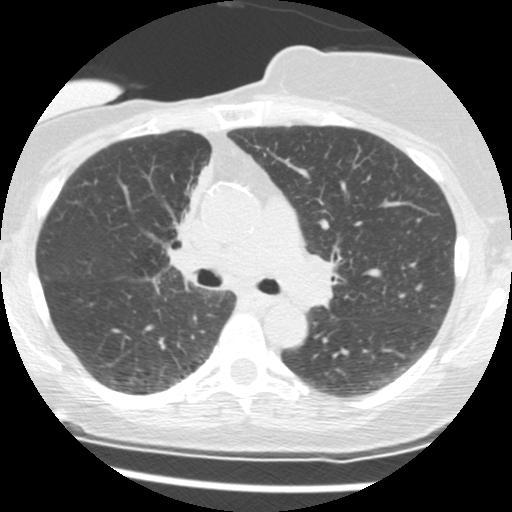
Chest CT (low-dose screening protocol), one axial image, second annual screen, lung window (W 1500 / L -600 HU), 2.5 mm slice thickness, standard (soft-tissue) reconstruction kernel (STANDARD). Female, age 56 years at enrolment. Current smoker at enrolment.
• Expert reader's lesion annotation, box from (x=152, y=163) to (x=207, y=257) px.
• The screening reader recorded 2 non-calcified nodules or masses ≥4 mm on this exam (right middle lobe, right lower lobe); which of them this box marks is not recorded.
• Official screen result: positive, change unspecified: nodule(s) >= 4 mm or enlarging nodule(s), mass(es), or other non-specific abnormalities suspicious for lung cancer.